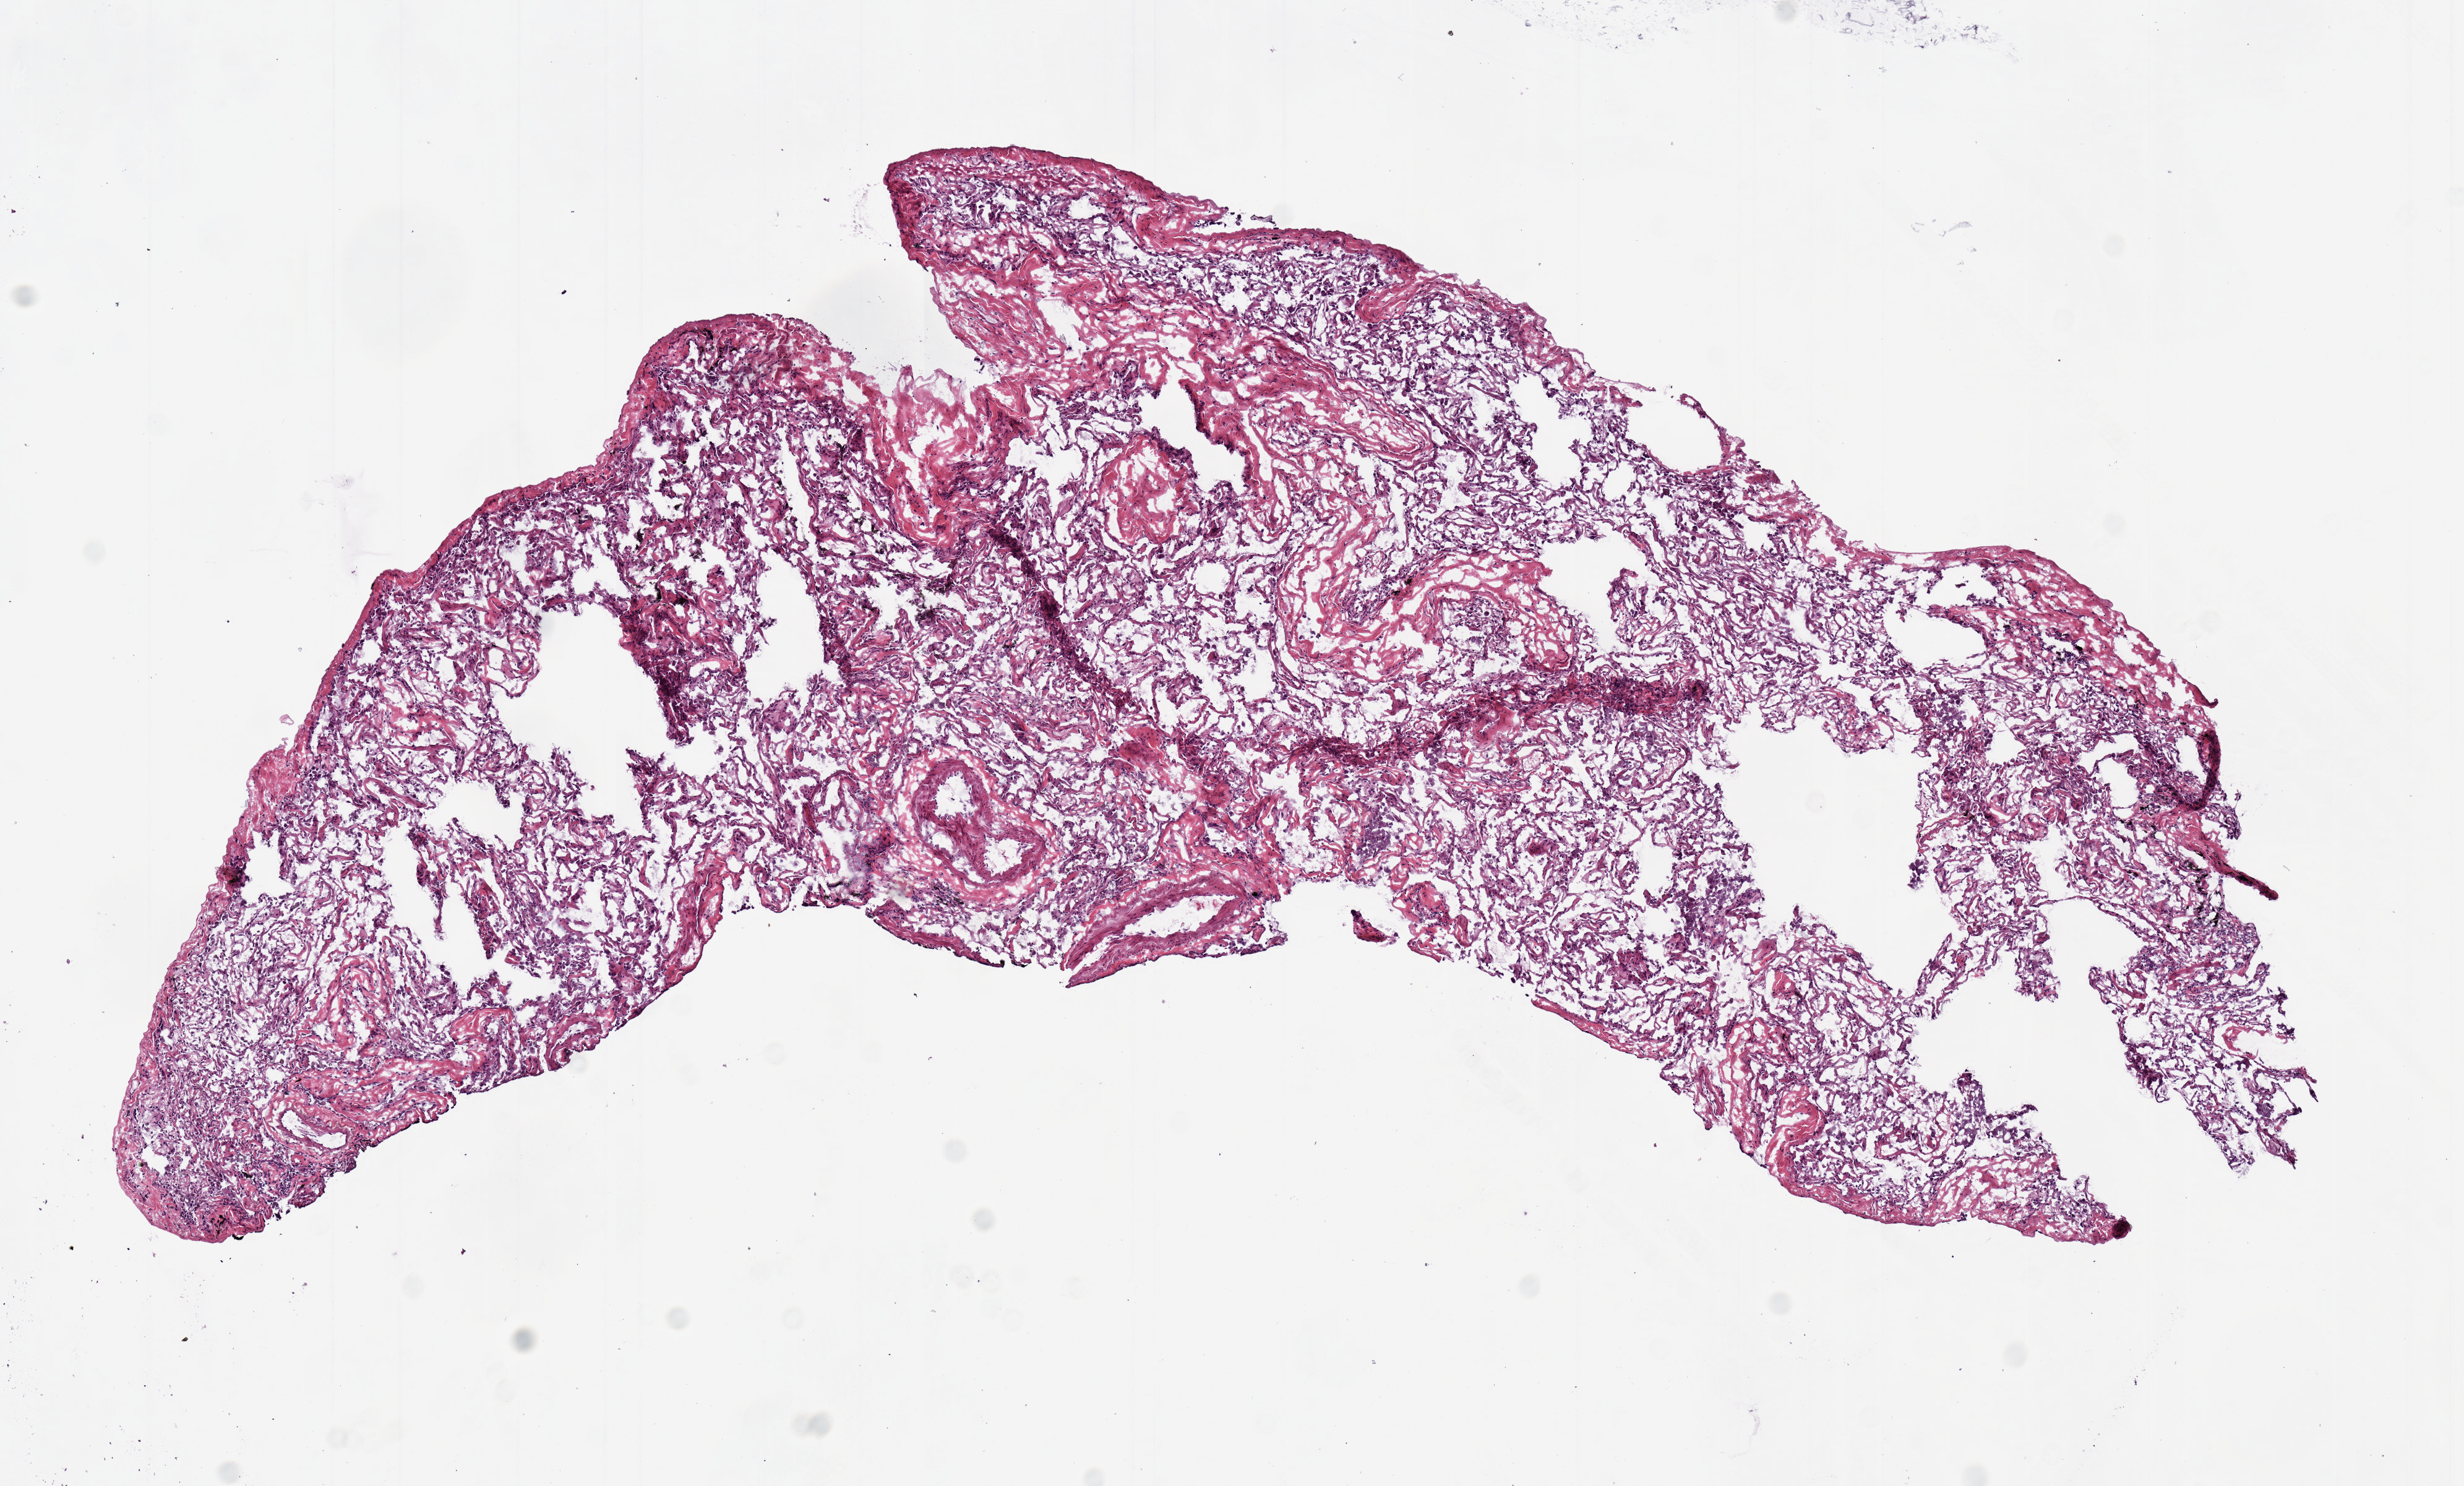
H&E whole-slide image, a low-resolution overview of the entire scanned area, about 7.9 x 4.7 mm (from a 20x scan), frozen section, lung, solid tissue normal (non-tumour tissue) sample. Patient: male, age at initial diagnosis 77 years.
- this section: solid tissue normal sample (biorepository sample class)
- patient diagnosis: Adenocarcinoma, NOS (lower lobe, lung)